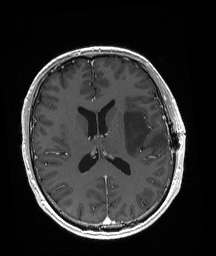
Brain MRI from a brain-tumour surgery series, one axial slice. Position 86 of 192 along the scan axis. T1-weighted post-contrast. 1 mm slice thickness. 216 × 256 image matrix. Case-level facts recorded for this patient, not image findings: histopathology: Astrocytoma; WHO grade: 3; IDH mutation: yes; tumour location: Left Posterior Frontal.
Annotated regions visible in this slice (outlined manually by an expert reader):
- tumour: box from (x=123, y=110) to (x=165, y=157) px